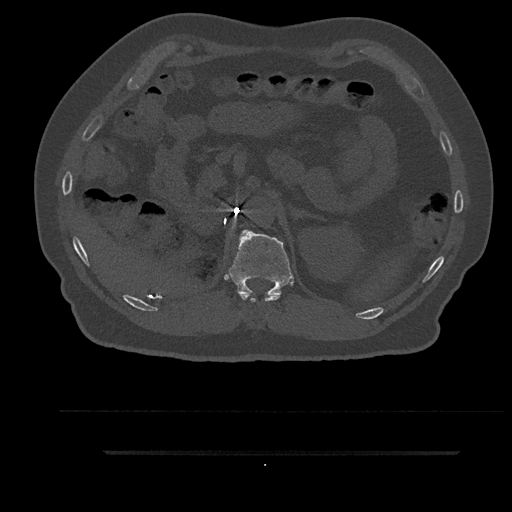
CT including the spine, one axial slice; position 263 of 797 along the scan axis; reconstruction kernel Br40s/3; bone window (W 1800 / L 400 HU); 512 × 512 image matrix. Male patient, age 63 years. From the clinical record (not read from this slice): primary cancer: renal; vertebrae with lytic lesions (as recorded): T8.
Annotated regions visible in this slice (semi-automatic segmentation, software-assisted and operator-edited):
- T11 vertebra: box from (x=240, y=294) to (x=281, y=302) px
- T12 vertebra: (x=228, y=229)–(x=294, y=295)